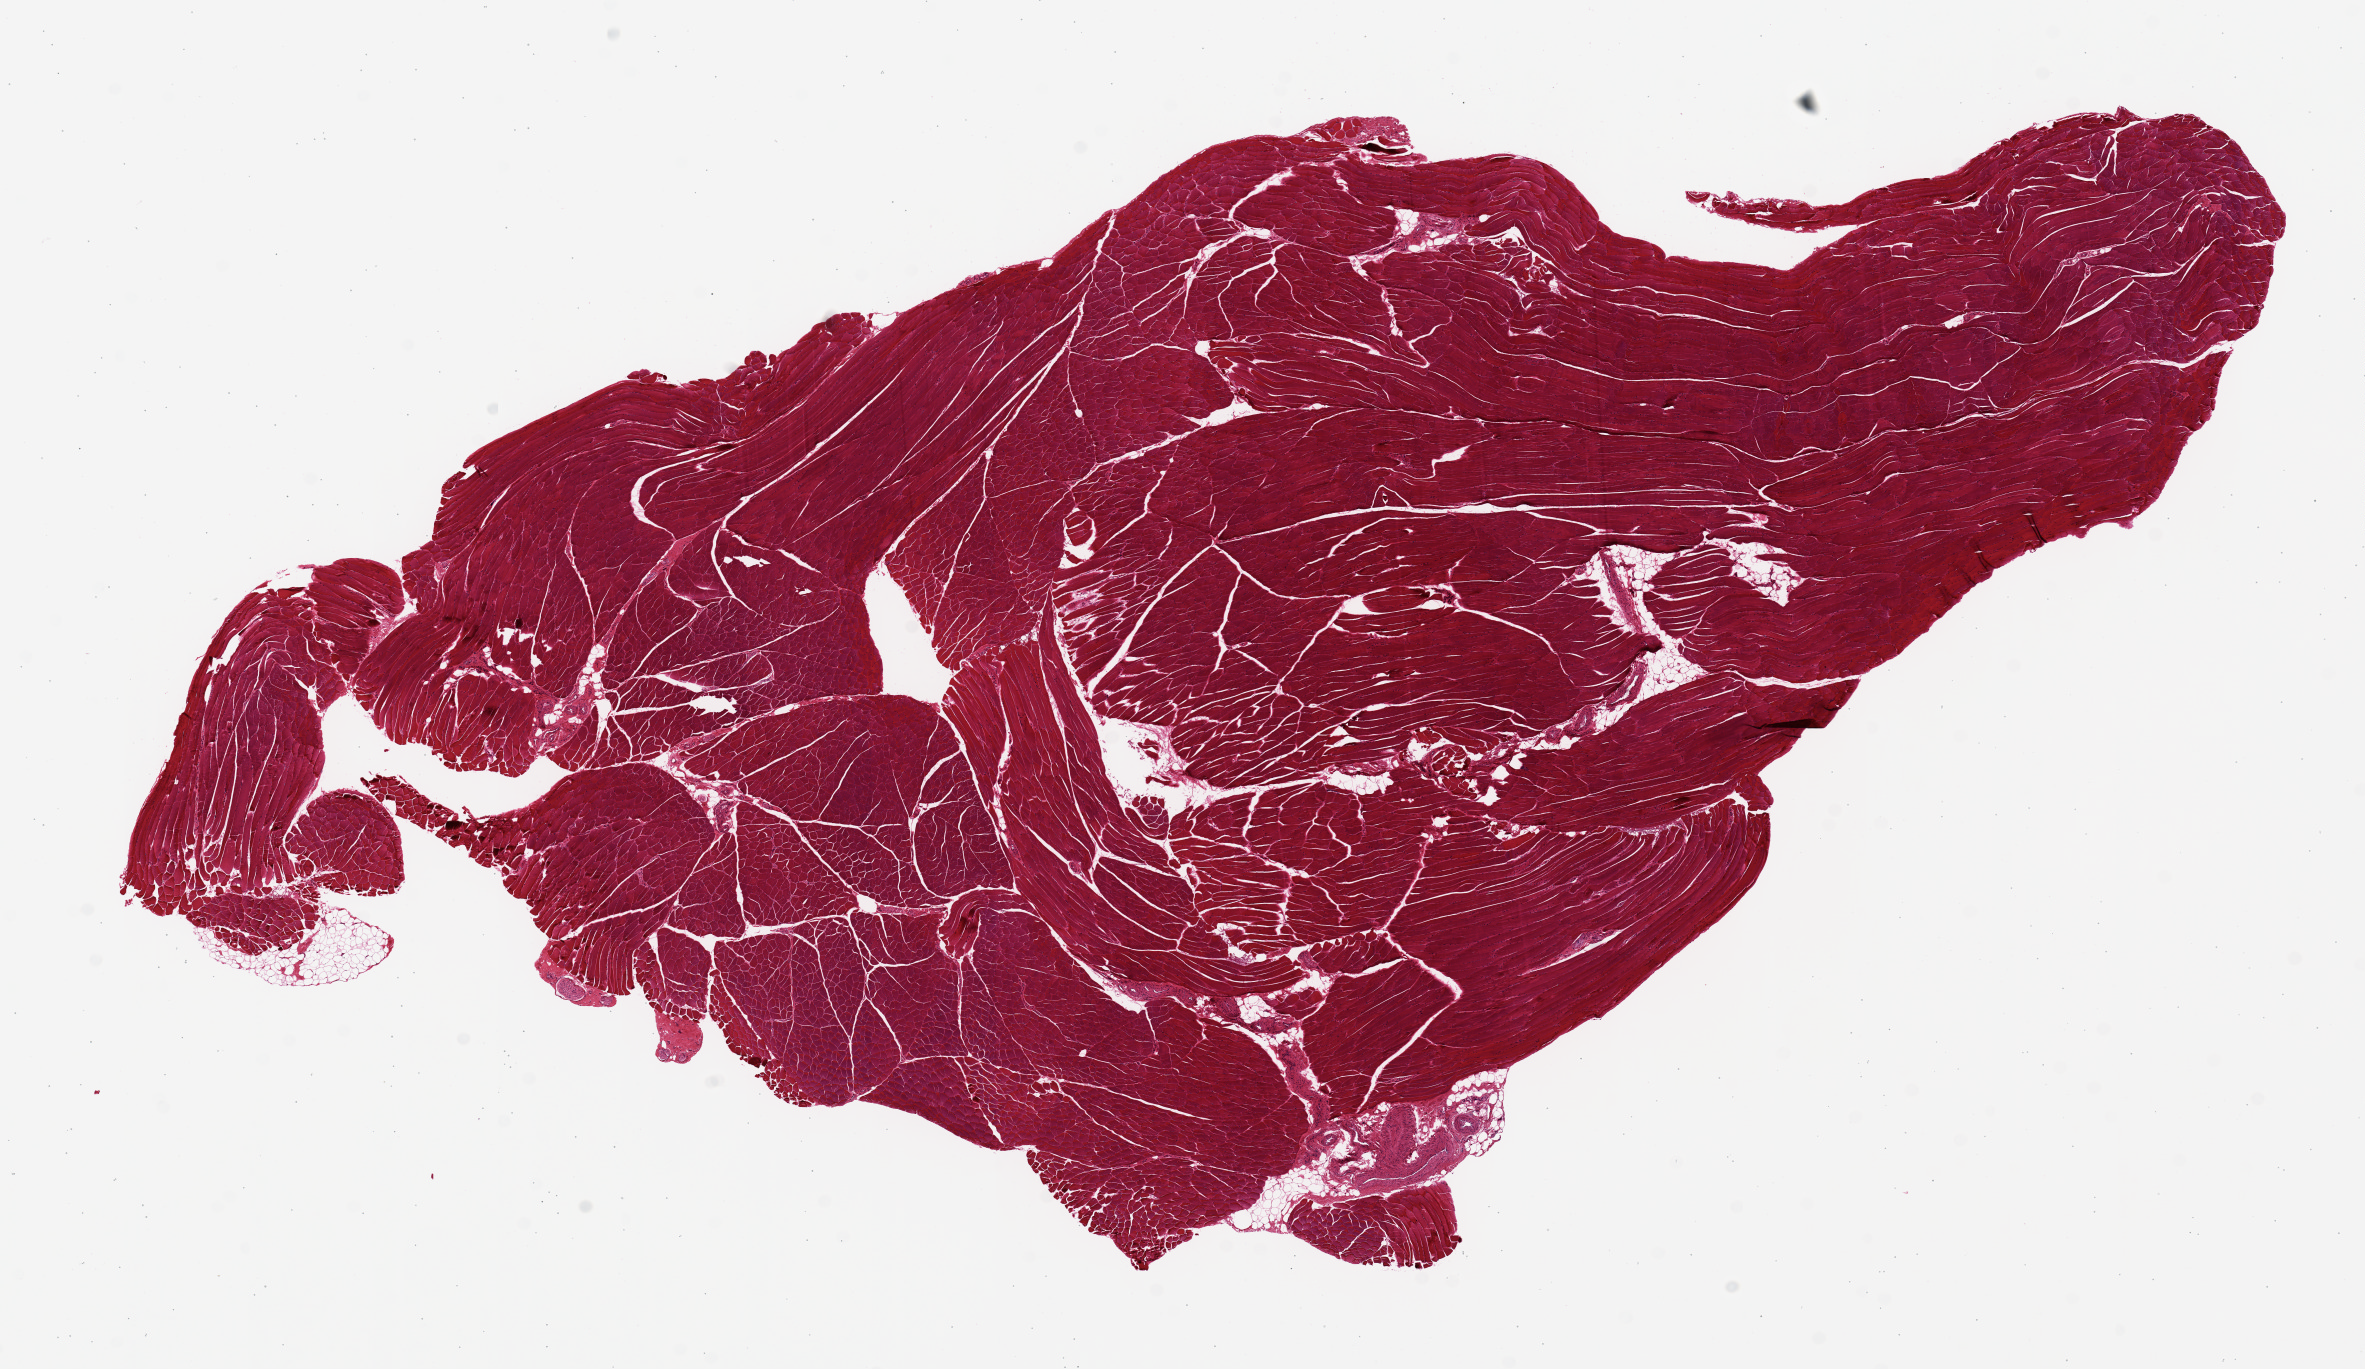
Digitized haematoxylin and eosin-stained section, shown as a low-resolution overview of the whole scanned area (about 18.7 x 10.8 mm, slide scanned at 20x), PAXgene-fixed paraffin-embedded (PFPE) section, section of skeletal muscle (target tissue), tissue donor sample. Donor: male.
Pathologist's review note for this sample: 17 x 9mm specimen, minimal fat.